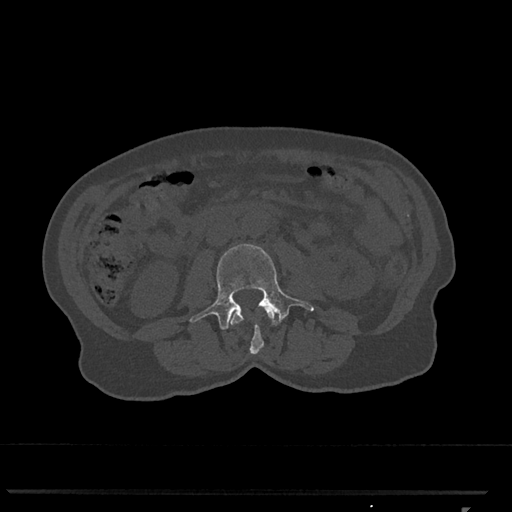
CT including the spine, one axial slice. Slice 289 of 793 in the series (ordered by position). Reconstruction kernel Br40s/3. Bone window (W 1800 / L 400 HU). 0.5 mm slice thickness. 512 × 512 image matrix, field of view 380 × 380 mm. Patient: female, 62 years. Case-level facts recorded for this patient, not image findings: primary cancer: renal.
Structures marked on this image (semi-automatic segmentation, software-assisted and operator-edited):
- L2 vertebra: bounding box [x1, y1, x2, y2] px = [229, 307, 279, 354]
- L3 vertebra: [190, 244, 314, 330]